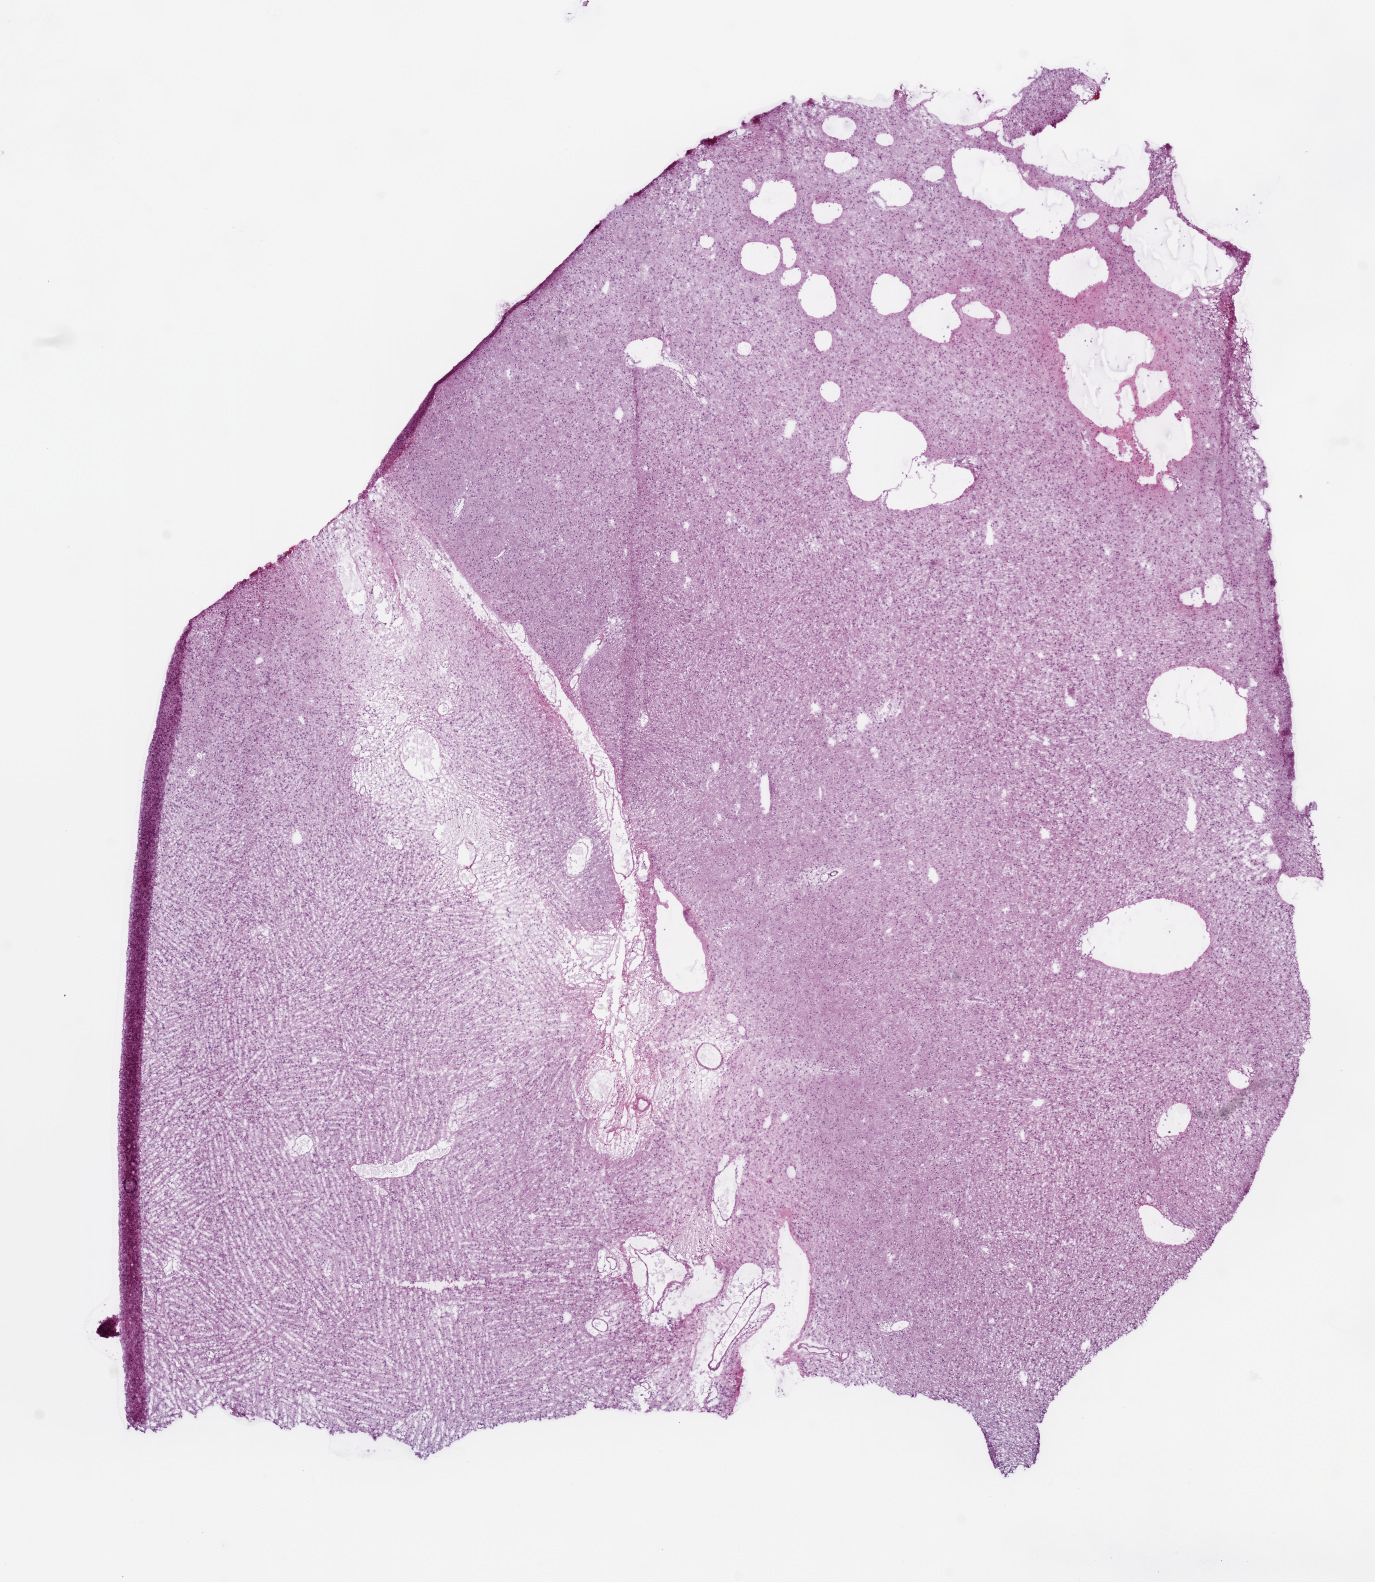
Digitized H&E tissue section (whole slide), shown as a low-resolution overview of the whole scanned area (about 11.0 x 12.7 mm, from a 20x scan). Frozen section from the top of the tissue portion. Sample: primary tumour, brain. Male patient; age at initial diagnosis 59 years. Histologic grade: G2 (moderately differentiated). Composition of this section per pathologist review: tumour cells 100%, tumour nuclei 60%, normal cells 0%, stromal cells 0%, necrosis 0%.
Histologic diagnosis: Oligodendroglioma, NOS (cerebrum).